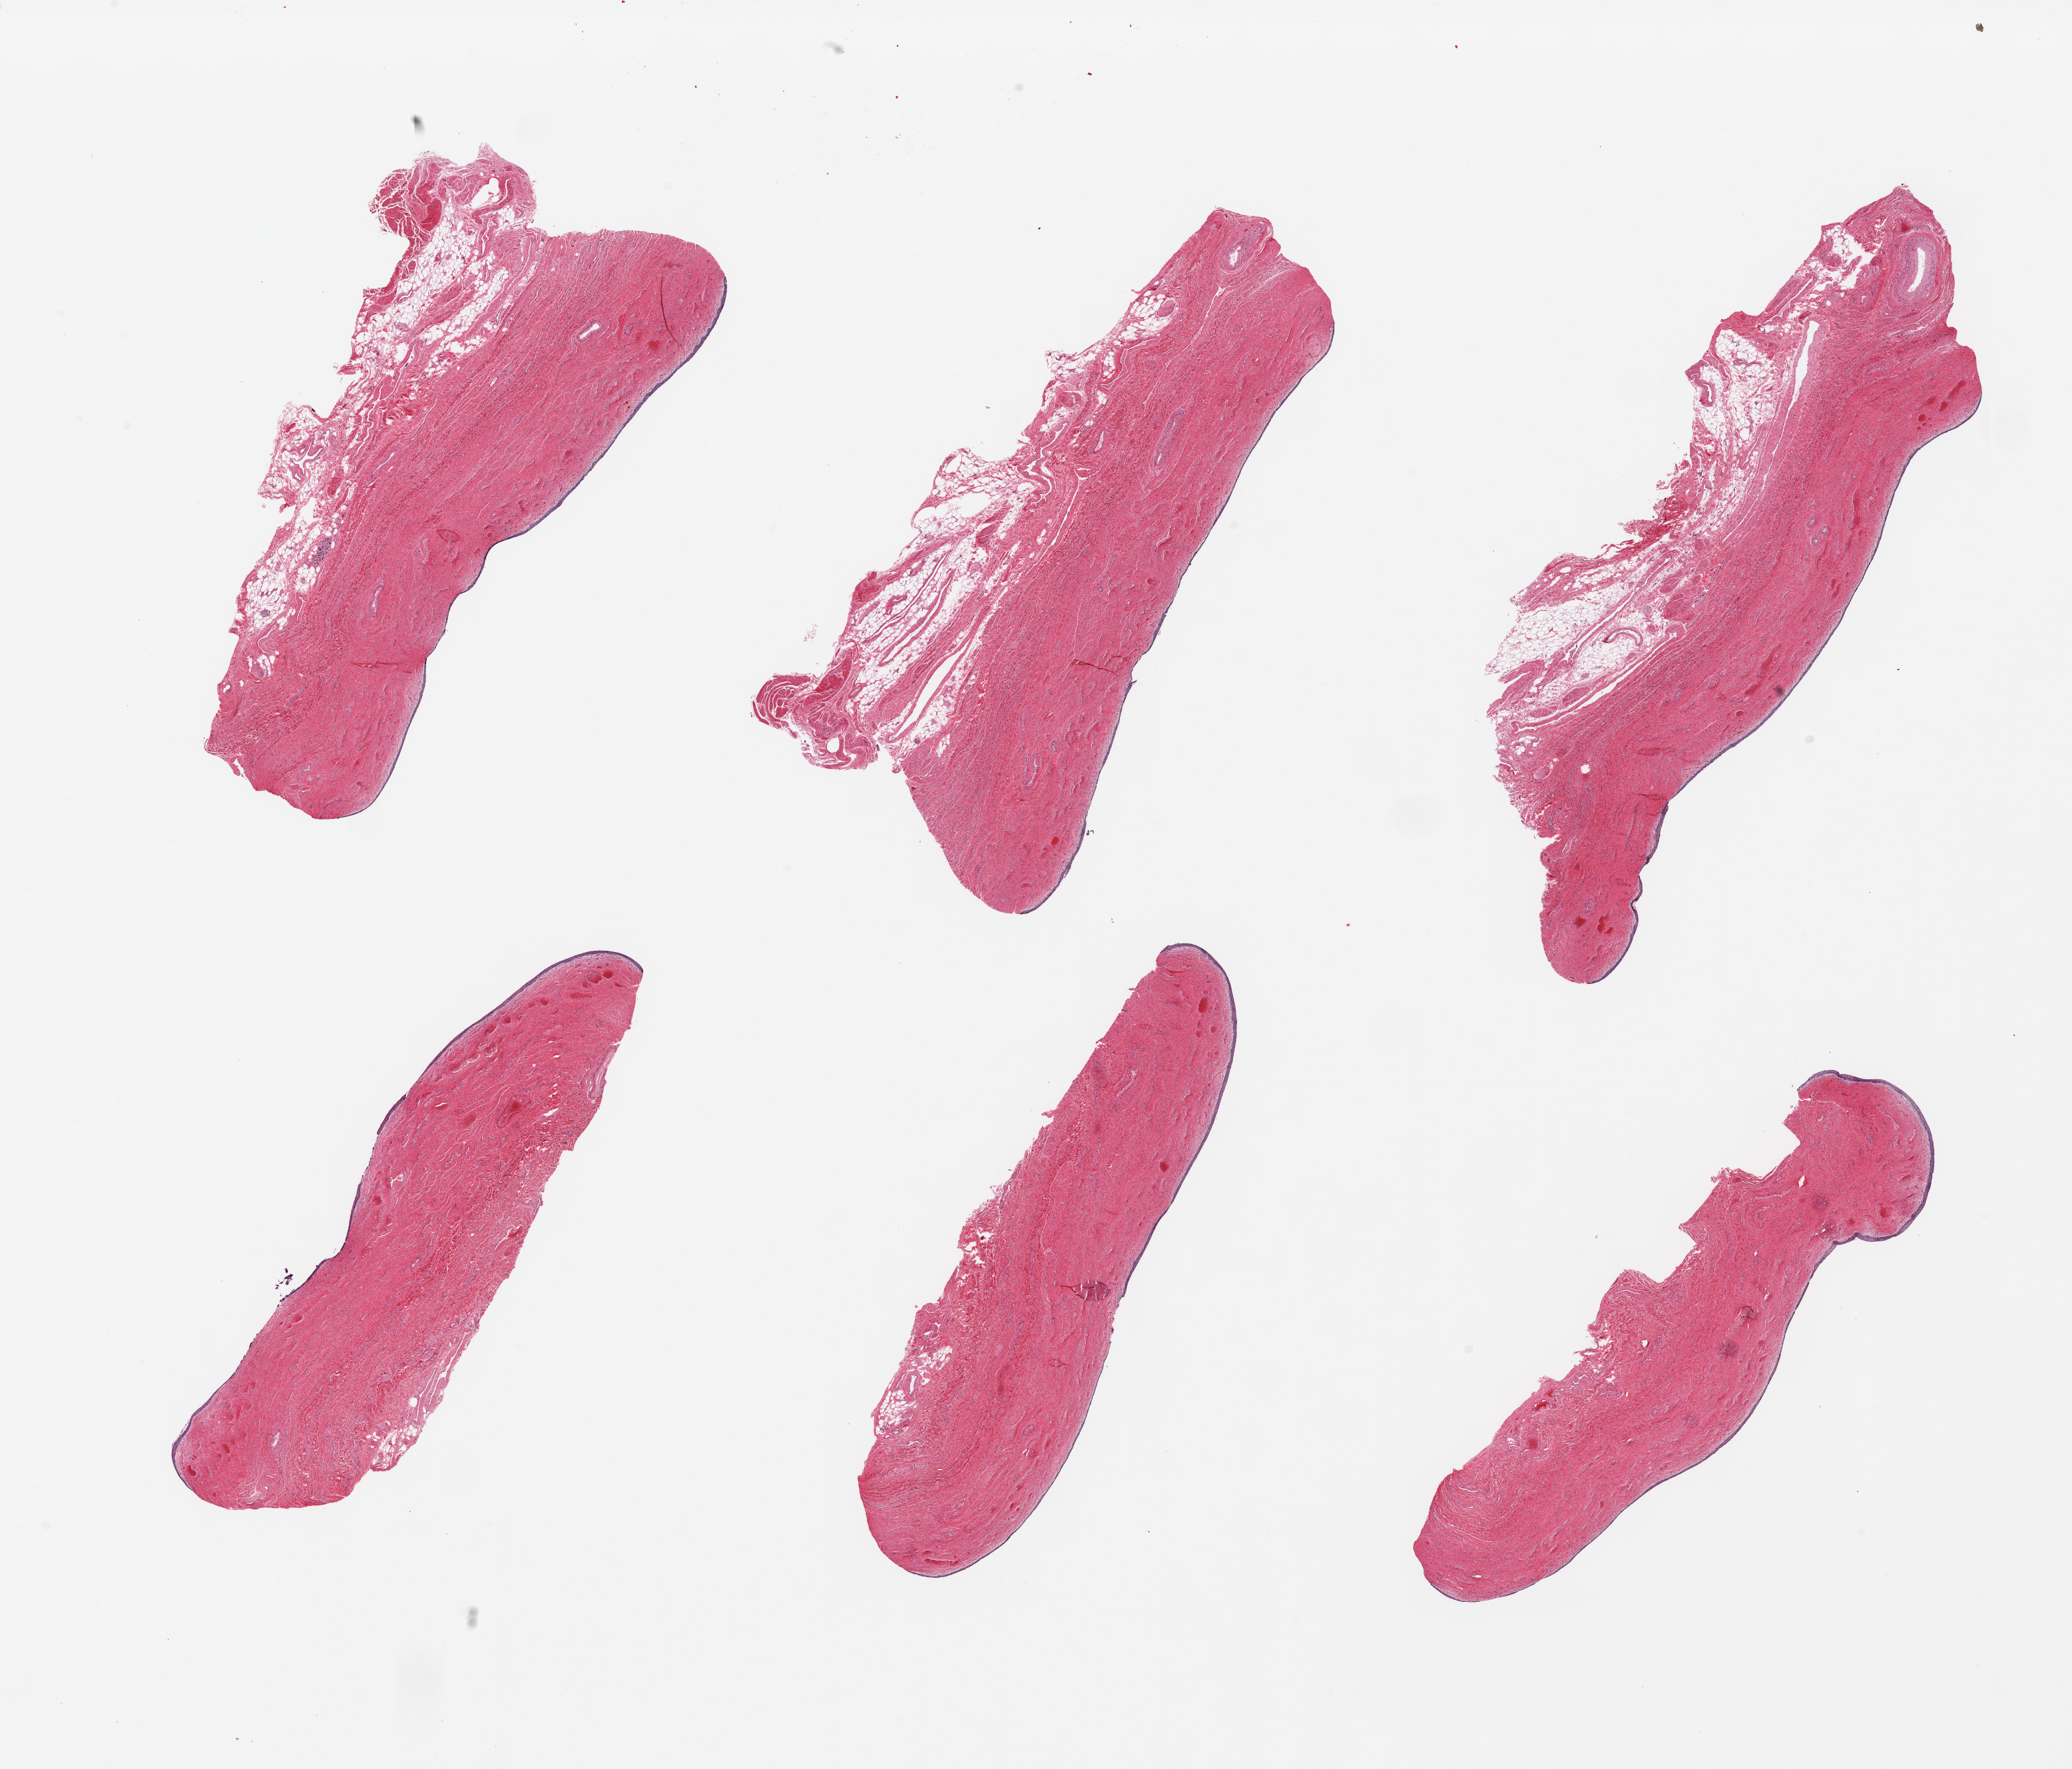
Digitized H&E-stained section, a low-resolution overview of the entire scanned area, about 24.6 x 21.0 mm (slide scanned at 20x), PAXgene-fixed paraffin-embedded (PFPE) section, target tissue: vagina, donor tissue sample. Donor sex: female.
* pathologist's review note for this sample: 2 pieces; atrophic, partially sloughed epithelium